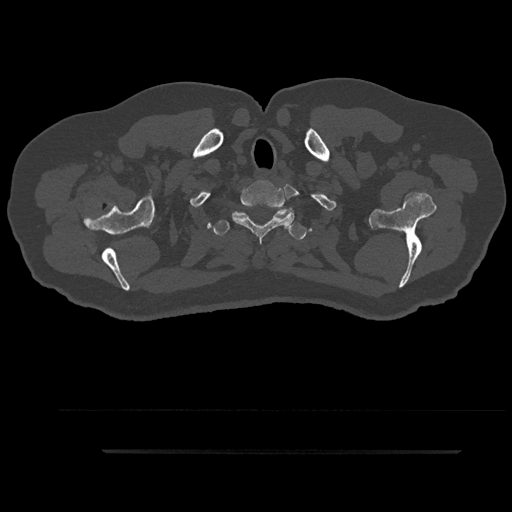
CT including the spine, one axial slice; position 787 of 797 along the scan axis; bone window (W 1800 / L 400 HU); 512 × 512 image matrix, field of view 432 × 432 mm. Patient: male, 63 years. Case-level facts recorded for this patient, not image findings: primary cancer: renal; vertebrae with lytic lesions (as recorded): T8.
Annotated regions visible in this slice (semi-automatic segmentation, software-assisted and operator-edited):
- T1 vertebra: bounding box (x1, y1, x2, y2) in pixels: (232, 185, 294, 243)
- T2 vertebra: (212, 207, 306, 240)